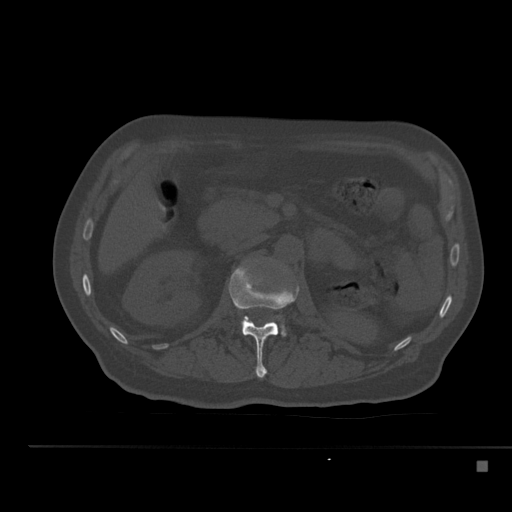
CT including the spine, one axial slice; reconstruction kernel Br40s; bone window (W 1800 / L 400 HU); 512 × 512 image matrix. Patient: male, 70 years. Case-level facts recorded for this patient, not image findings: primary cancer: renal.
Annotated regions visible in this slice (semi-automatically segmented with operator editing):
- L1 vertebra: bounding box (x1, y1, x2, y2) in pixels: (229, 261, 299, 378)
- L2 vertebra: (282, 327, 286, 336)